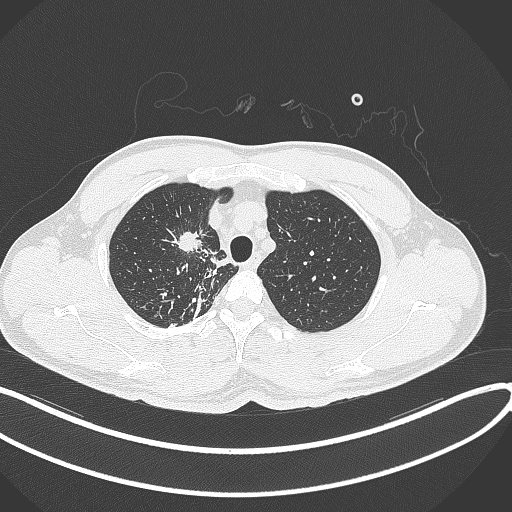
Chest CT, one axial slice. Position 307 of 391 along the scan axis. Reconstruction kernel B70f. Lung window (W 1500 / L -600 HU). 1 mm slice thickness. 512 × 512 image matrix. Male patient, age 48 years. From the clinical record (not read from this slice): clinical TNM (as recorded): T1c N1 M1.
Annotated regions visible in this slice (rectangle marked by the reading radiologist):
- lung tumour (recorded histology: adenocarcinoma): bounding box [x1, y1, x2, y2] px = [170, 227, 206, 261]